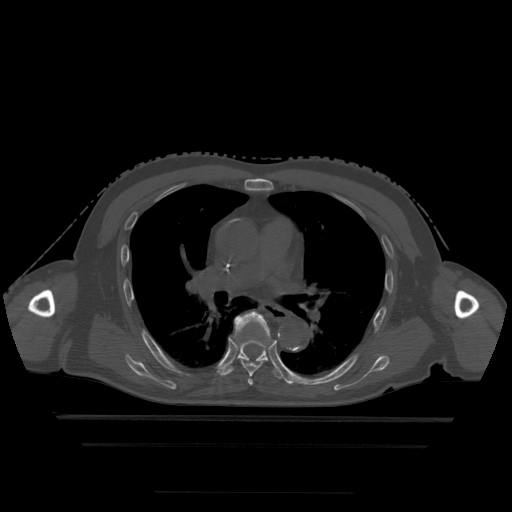
CT including the spine, one axial slice; slice 310 of 522 in the series (ordered by position); bone window (W 1800 / L 400 HU); 1.25 mm slice thickness; 512 × 512 image matrix, field of view 436 × 436 mm. Patient age 68 years. Case-level facts recorded for this patient, not image findings: primary cancer: urothelial.
Annotated regions visible in this slice (semi-automatically segmented with operator editing):
- T5 vertebra: box from (x=248, y=376) to (x=253, y=386) px
- T6 vertebra: (x=235, y=311)–(x=272, y=376)
- T7 vertebra: (x=221, y=341)–(x=287, y=382)